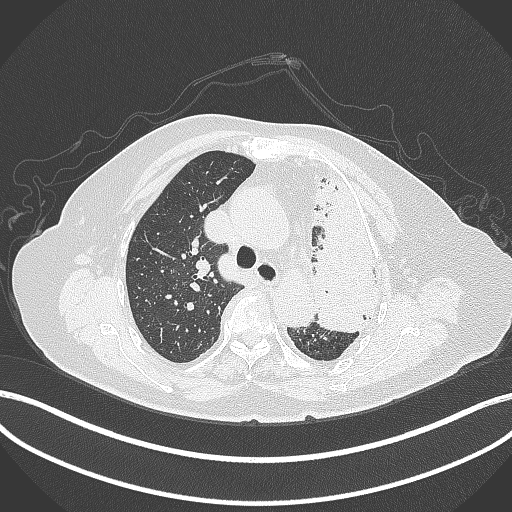
Chest CT, one axial slice. Position 280 of 399 along the scan axis. 120 kVp. Lung window (W 1500 / L -600 HU). 1 mm slice thickness. 512 × 512 image matrix, field of view 400 × 400 mm. Patient: female, 75 years. From the clinical record (not read from this slice): clinical TNM (as recorded): T3 N3 M1.
Outlined on this slice (rectangle marked by the reading radiologist):
- lung tumour (recorded histology: adenocarcinoma): bounding box (x1, y1, x2, y2) in pixels: (308, 164, 384, 333)